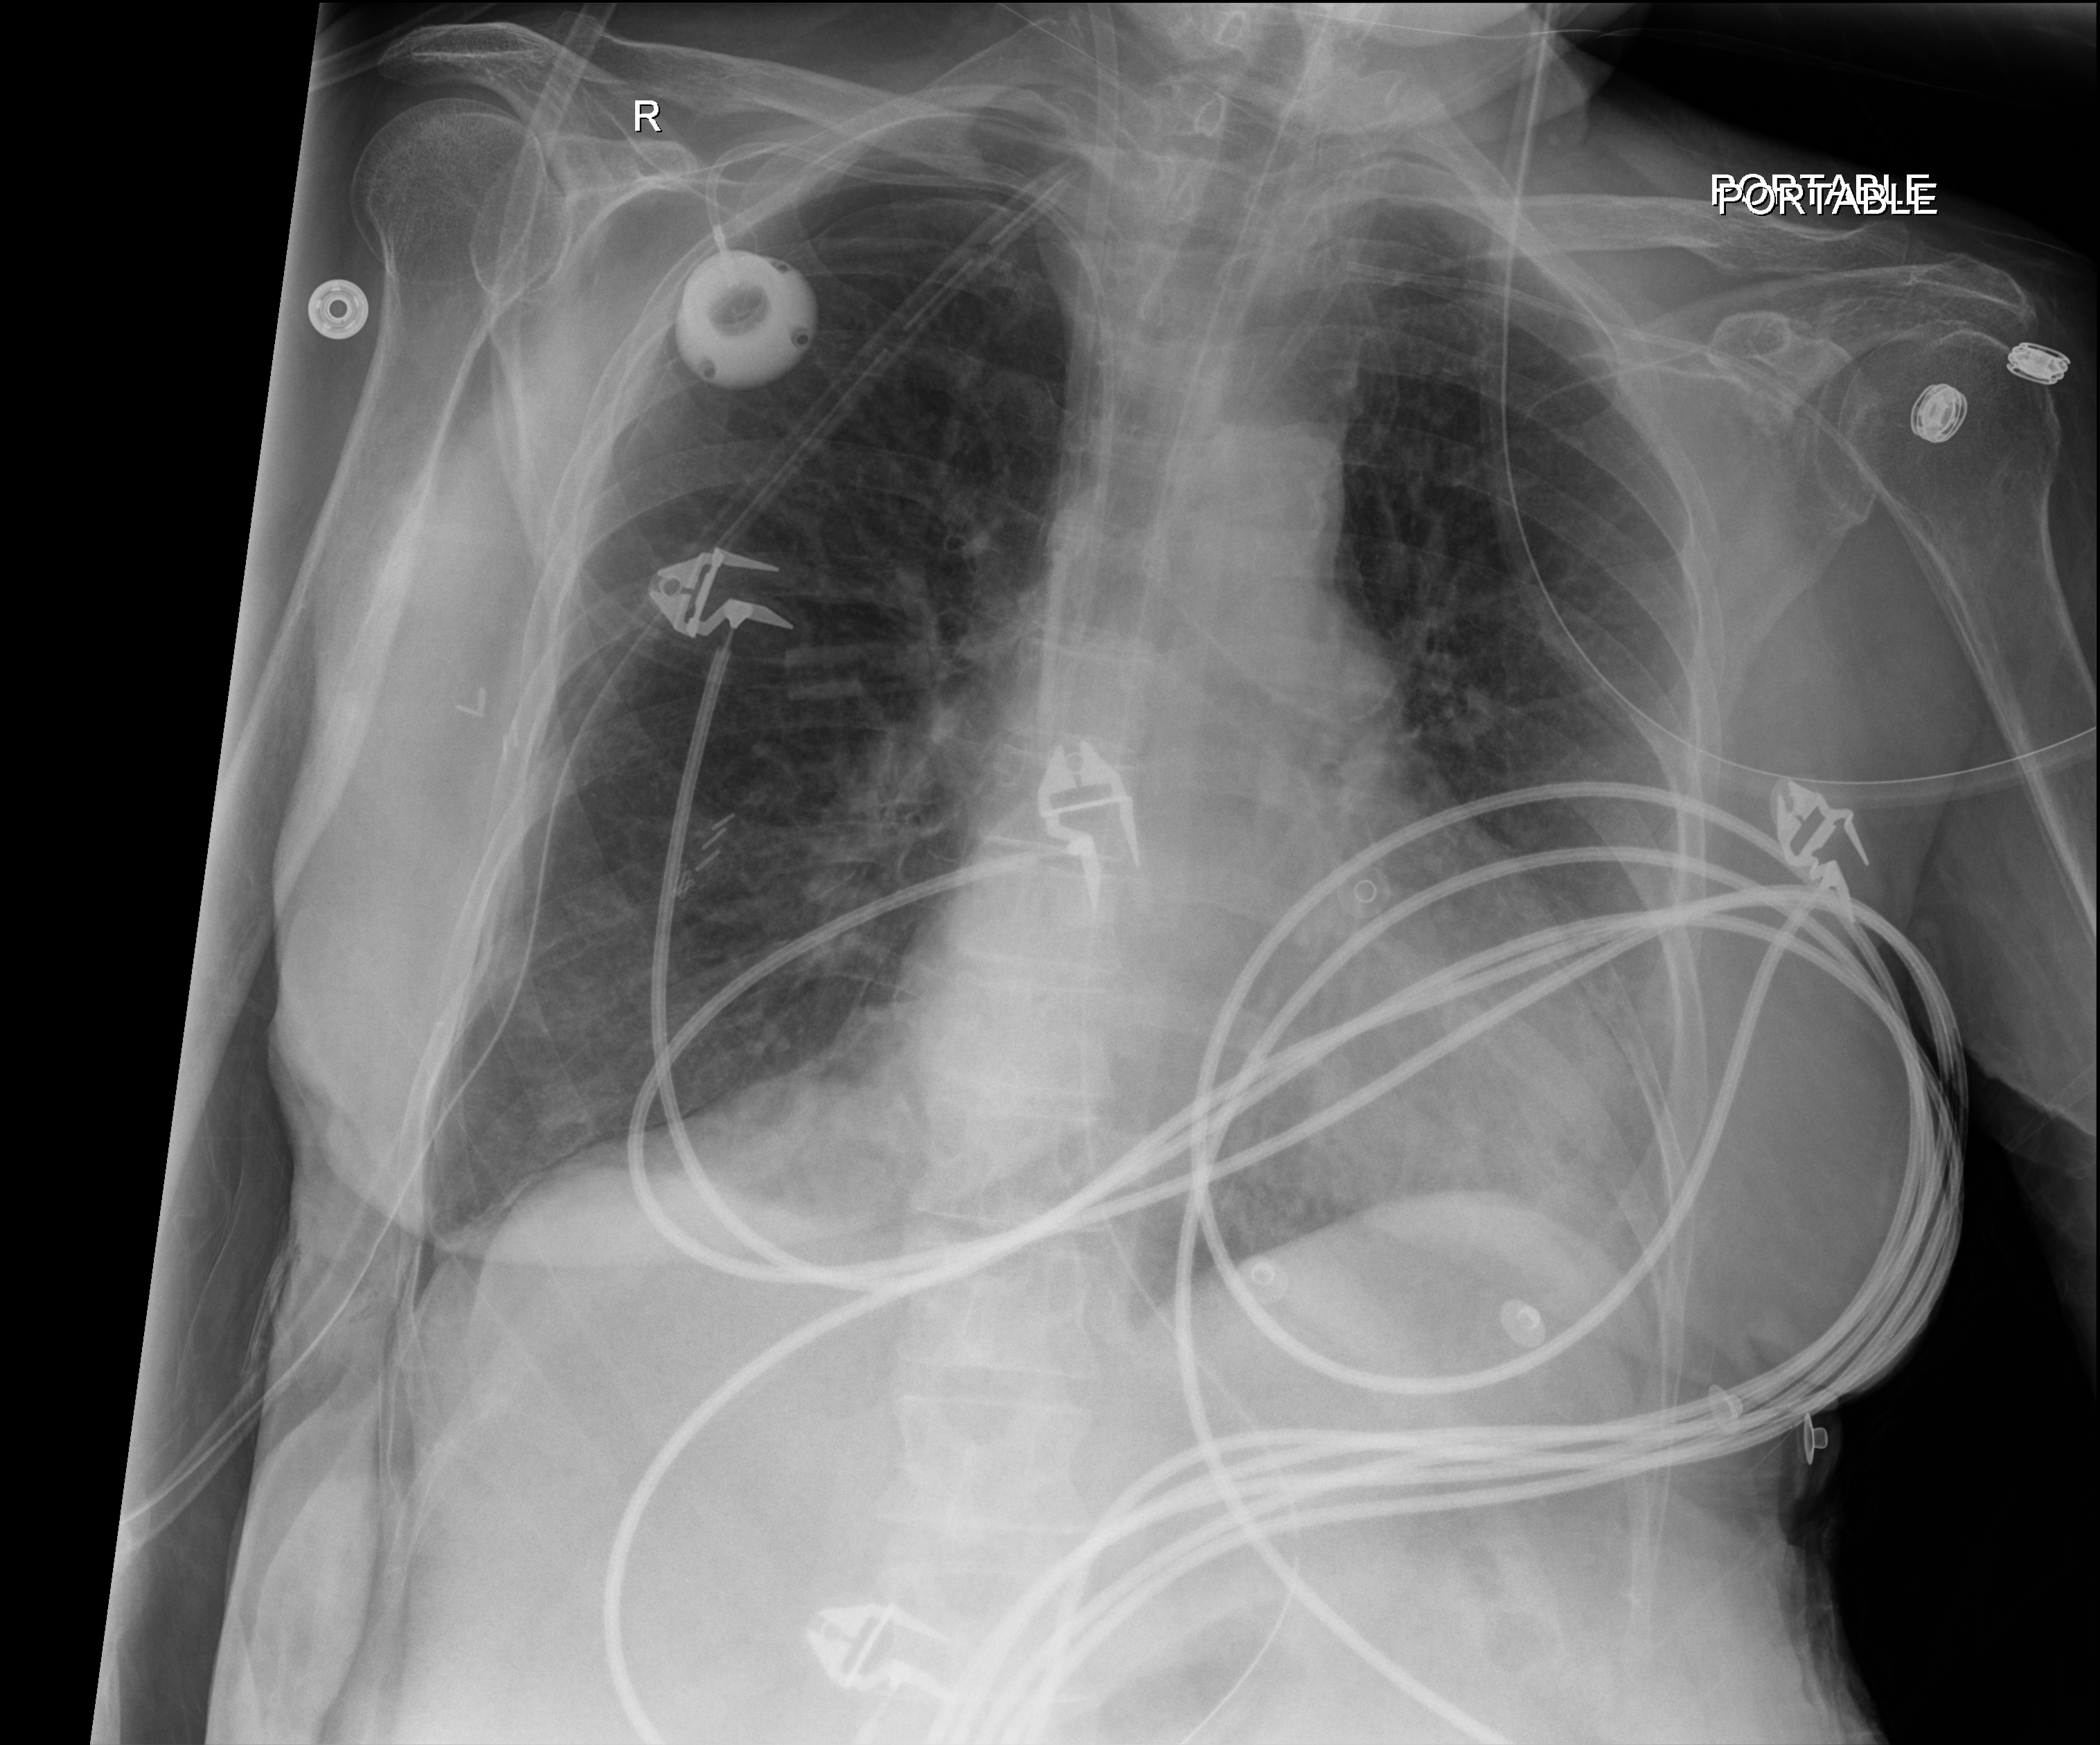
Chest radiograph (digital radiography); anteroposterior (AP) projection. Patient hospitalised with COVID-19; female, aged 60–74 years.
Admission-level facts for this patient (not findings on this image; timing relative to this image not recorded):
- admitted to intensive care during this hospital stay: yes